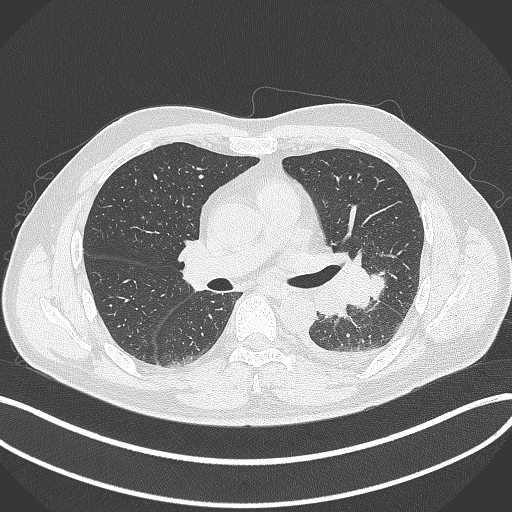
Chest CT, one axial slice; slice 204 of 342 in the series (ordered by position); reconstruction kernel B70f; 120 kVp; lung window (W 1500 / L -600 HU); 1 mm slice thickness; 512 × 512 image matrix. Male patient, age 58 years. From the clinical record (not read from this slice): clinical TNM (as recorded): T3 N1 M1b.
Structures marked on this image (bounding box drawn by a radiologist):
- lung tumour (recorded histology: small cell carcinoma): bounding box (x1, y1, x2, y2) in pixels: (348, 251, 389, 312)